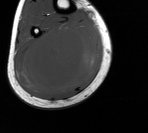
MRI of an extremity soft-tissue mass, one axial slice; slice 56 of 76 in the series (ordered by position); MR volume resampled by the dataset authors to the PET/CT grid (not the native acquisition matrix); 3.27 mm slice thickness; 148 × 133 image matrix, field of view 145 × 130 mm. Male patient. Case-level facts recorded for this patient, not image findings: histological type: liposarcoma - round cell; grade: high; site of the primary tumour: right calf.
Outlined on this slice (expert contour drawn on MRI and transferred to this co-registered scan by the dataset authors):
- gross tumour volume (mass): bounding box <15,19,101,97> (left, top, right, bottom; pixels)